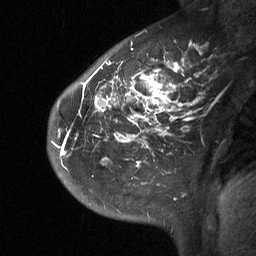
Breast MRI (dynamic contrast-enhanced), one sagittal slice. Position 43 of 64 along the scan axis. Dynamic contrast-enhanced study with each time point stored as its own series, time point 2 of 3 at this slice position (early post-contrast, ordered by acquisition time). 1.5 T. TE 4.8 ms, TR 27 ms. 2 mm slice thickness. 256 × 256 image matrix, field of view 200 × 200 mm. Patient: female, 42 years. From the clinical record (not read from this slice): setting: breast cancer imaged before/during neoadjuvant chemotherapy; receptor status: triple-negative.
Outlined on this slice (semi-automatic segmentation, software-assisted and operator-edited):
- analysis volume of interest (the breast-tissue region the enhancement analysis was run in; not a lesion): box from (x=48, y=29) to (x=202, y=190) px
- tumour enhancement mask (voxels above the 90 % enhancement threshold inside the analysis volume of interest): (x=60, y=59)–(x=183, y=163)